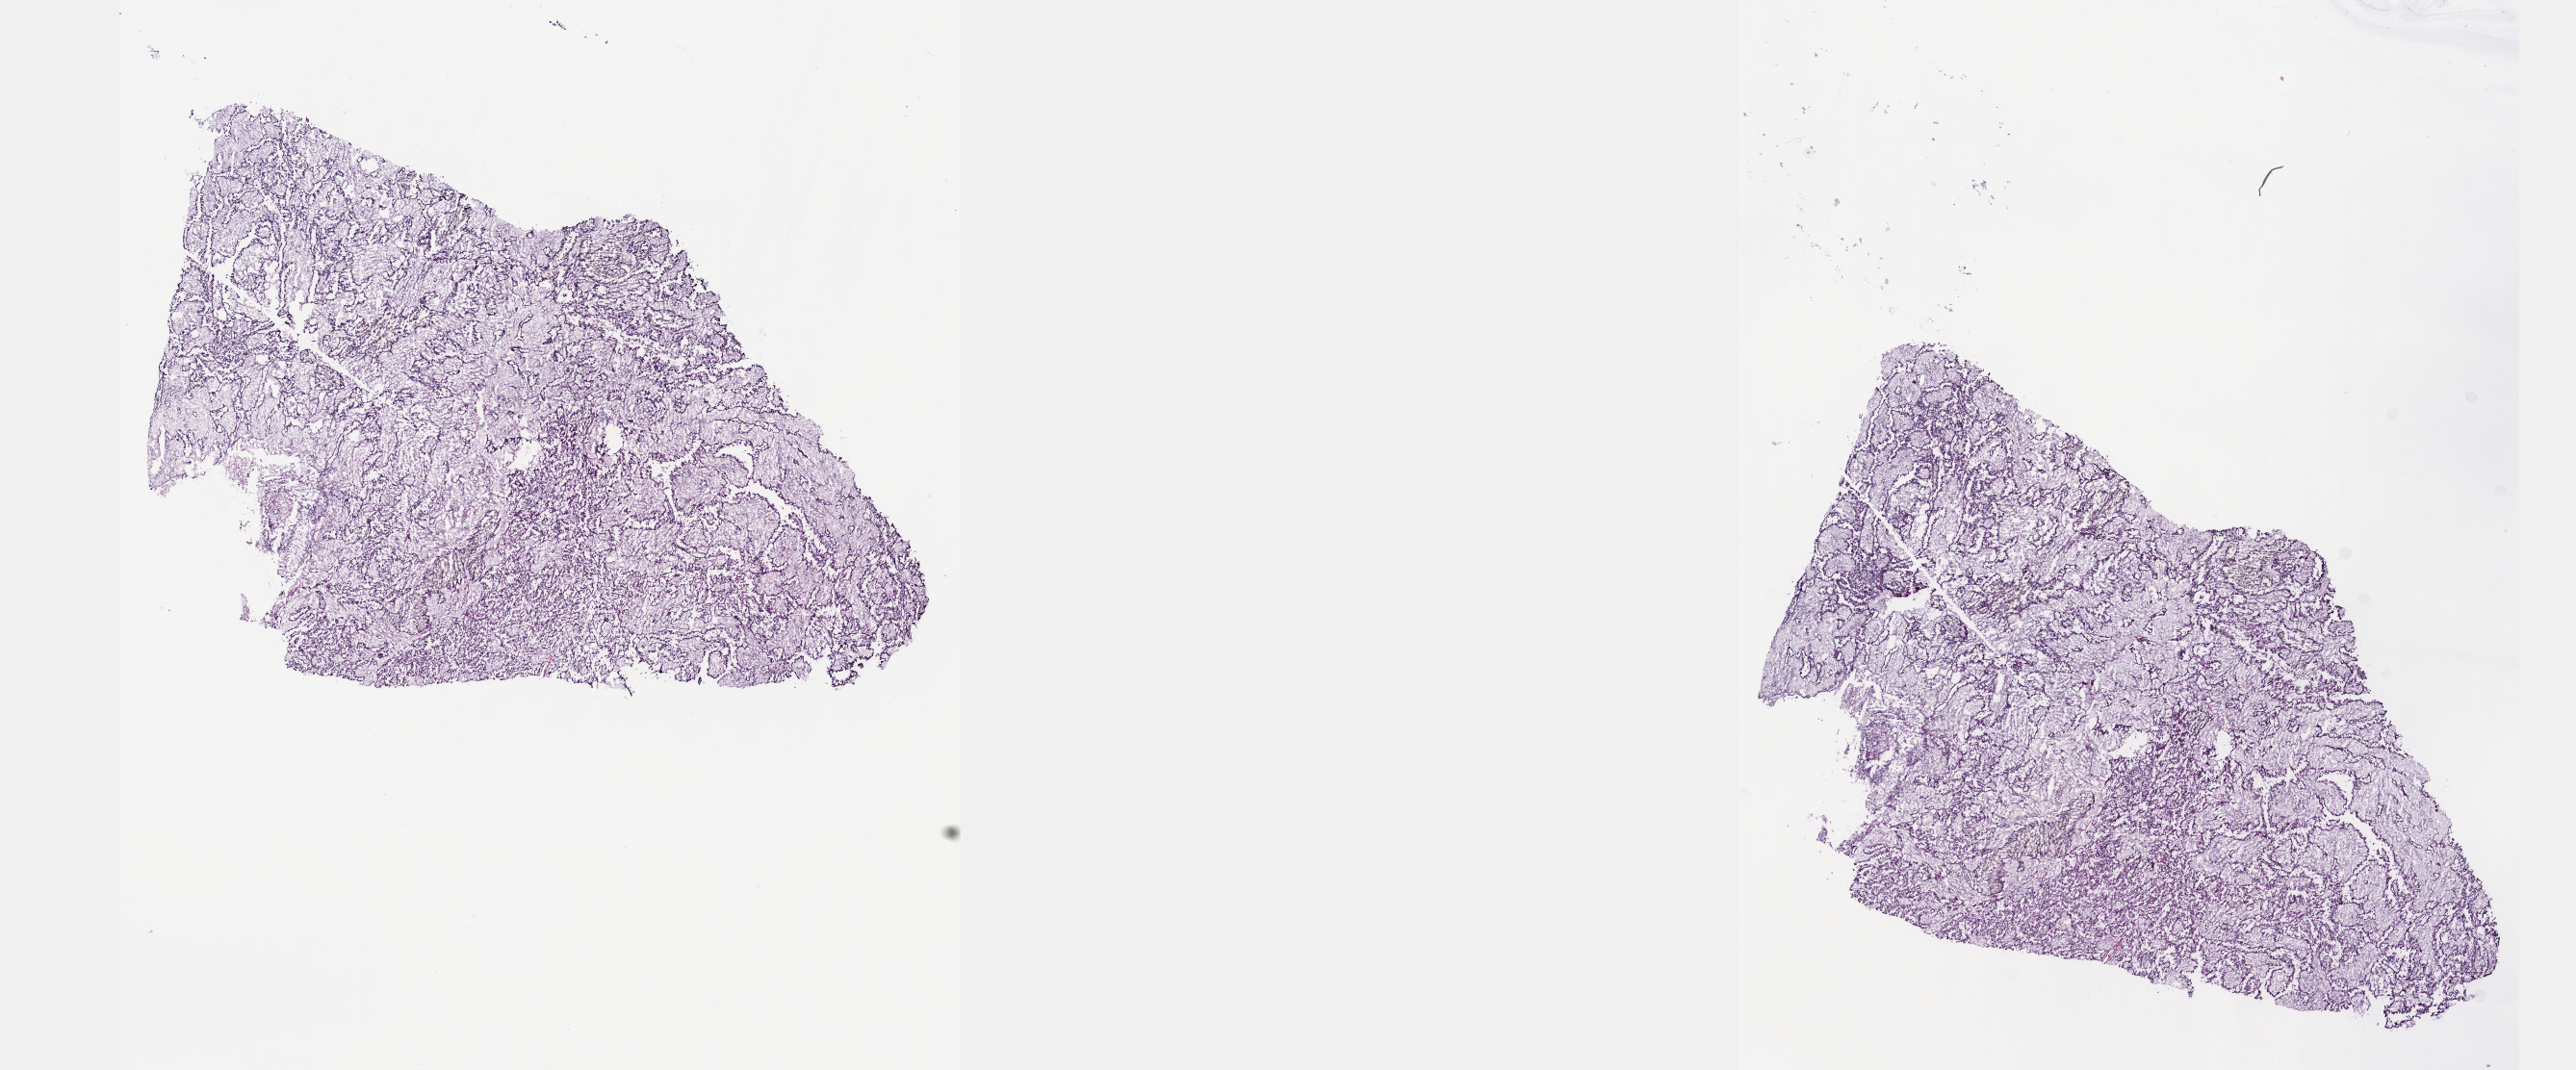
Digitized Hematoxylin and eosin (H&E) stained tissue section (whole slide), shown as a low-resolution overview of the whole scanned area (about 21.6 x 9.0 mm). Frozen section from the top of the tissue portion. Sample: primary tumour, kidney. Male, age 71 years at initial diagnosis. Composition of this section per pathologist review: tumour cells 100%, tumour nuclei 80%, normal cells 0%, stromal cells 0%, necrosis 0%. Infiltration values recorded for this section: lymphocyte infiltration 1%, monocyte infiltration 3%, neutrophil infiltration 0%.
Diagnosis: Papillary adenocarcinoma, NOS. AJCC pathologic stage: I.